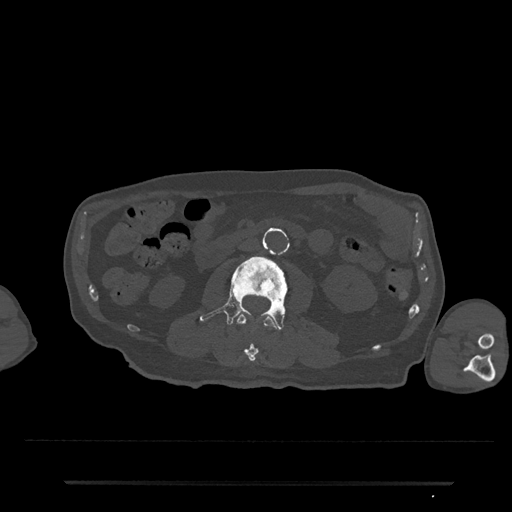
CT including the spine, one axial slice; slice 9 of 797 in the series (ordered by position); 120 kVp; bone window (W 1800 / L 400 HU); 0.5 mm slice thickness; 512 × 512 image matrix, field of view 427 × 427 mm. Male patient, age 74 years. Case-level facts recorded for this patient, not image findings: primary cancer: prostate.
Outlined on this slice (semi-automatic segmentation, software-assisted and operator-edited):
- L2 vertebra: bounding box [x1, y1, x2, y2] px = [235, 314, 279, 362]
- L3 vertebra: [200, 256, 304, 330]